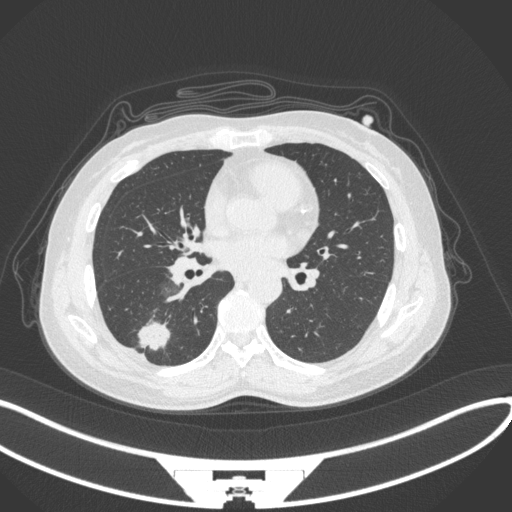
Chest CT, one axial slice; slice 142 of 352 in the series (ordered by position); reconstruction kernel B31f; lung window (W 1500 / L -600 HU); 512 × 512 image matrix, field of view 400 × 400 mm. Patient: female, 55 years. From the clinical record (not read from this slice): clinical TNM (as recorded): T1c N1 M0.
Outlined on this slice (bounding box drawn by a radiologist):
- lung tumour (recorded histology: adenocarcinoma): box from (x=138, y=314) to (x=176, y=357) px